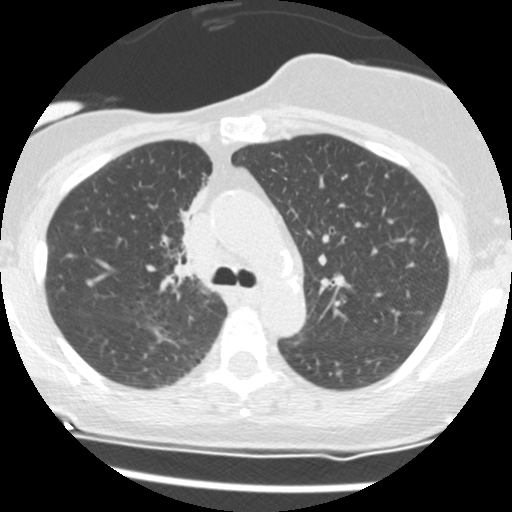
Chest CT (low-dose screening protocol), one axial image. Second screening round (one year after baseline). Lung window (W 1500 / L -600 HU). Slice 44 of 165 in the series. Female participant, aged 56 years at enrolment. Current smoker at enrolment.
Expert-annotated lung lesion, bounding box <153,186,211,270> (left, top, right, bottom; pixels). The screening reader recorded 2 non-calcified nodules or masses ≥4 mm on this exam (right middle lobe, right lower lobe); which of them this box marks is not recorded. Official screen result: positive, change unspecified: nodule(s) >= 4 mm or enlarging nodule(s), mass(es), or other non-specific abnormalities suspicious for lung cancer. Lung cancer was diagnosed 675 days after this screen (after the third annual screen): adenocarcinoma, NOS, right upper lobe, stage IIIB (AJCC 6th edition), 8 mm at pathology.